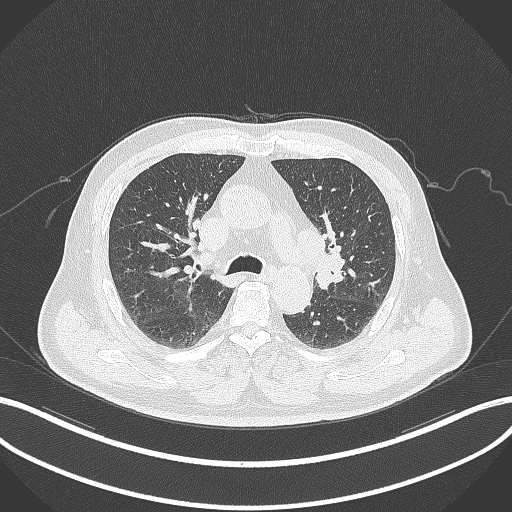
Chest CT, one axial slice; position 194 of 286 along the scan axis; reconstruction kernel B70f; 120 kVp; lung window (W 1500 / L -600 HU); 512 × 512 image matrix. Male patient, age 67 years. From the clinical record (not read from this slice): clinical TNM (as recorded): T2a N1 M0; histopathological grade: G3.
Annotated regions visible in this slice (rectangle marked by the reading radiologist):
- lung tumour (recorded histology: adenocarcinoma): bounding box (x1, y1, x2, y2) in pixels: (323, 241, 348, 285)